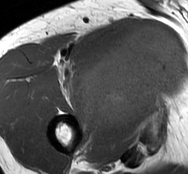
MRI of an extremity soft-tissue mass, one axial slice; position 57 of 93 along the scan axis; MR volume resampled by the dataset authors to the PET/CT grid (not the native acquisition matrix); 3.27 mm slice thickness; 188 × 174 image matrix, field of view 184 × 170 mm. Male patient. From the clinical record (not read from this slice): histological type: undifferentiated - pleiomorphic; grade: high; site of the primary tumour: right thigh.
Annotated regions visible in this slice (expert contour drawn on MRI and transferred to this co-registered scan by the dataset authors):
- gross tumour volume including surrounding oedema: bounding box [x1, y1, x2, y2] px = [77, 24, 185, 129]
- gross tumour volume (mass): [77, 24, 185, 129]